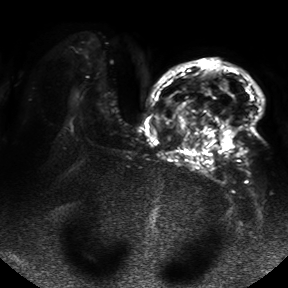
Breast MRI, one axial slice; slice 28 of 50 in the series (ordered by position); diffusion-weighted series; image 2 of 4 stored at this slice position (different b-values; order by instance number); 1.5 T; 4 mm slice thickness; 288 × 288 image matrix, field of view 390 × 390 mm. Female patient.
Annotated regions visible in this slice (manually delineated by an expert):
- tumour on diffusion-weighted imaging: bounding box [x1, y1, x2, y2] px = [220, 130, 236, 150]